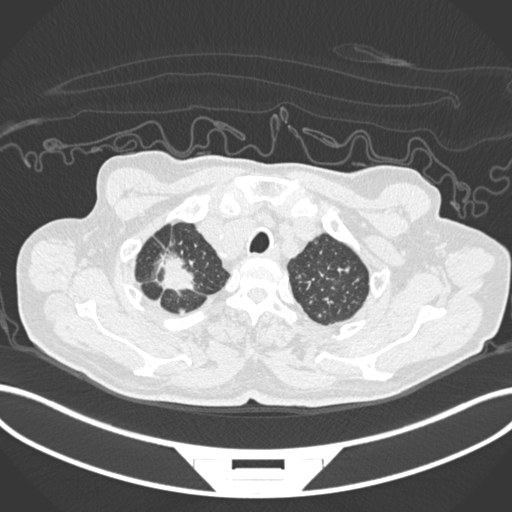
Chest CT, one axial slice; position 195 of 207 along the scan axis; reconstruction kernel B30f; 120 kVp; lung window (W 1500 / L -600 HU); 1 mm slice thickness; 512 × 512 image matrix, field of view 400 × 400 mm. Male patient, age 69 years. Case-level facts recorded for this patient, not image findings: clinical TNM (as recorded): T1c N1 M1.
Outlined on this slice (rectangle marked by the reading radiologist):
- lung tumour (recorded histology: adenocarcinoma): bounding box [x1, y1, x2, y2] px = [152, 243, 204, 297]